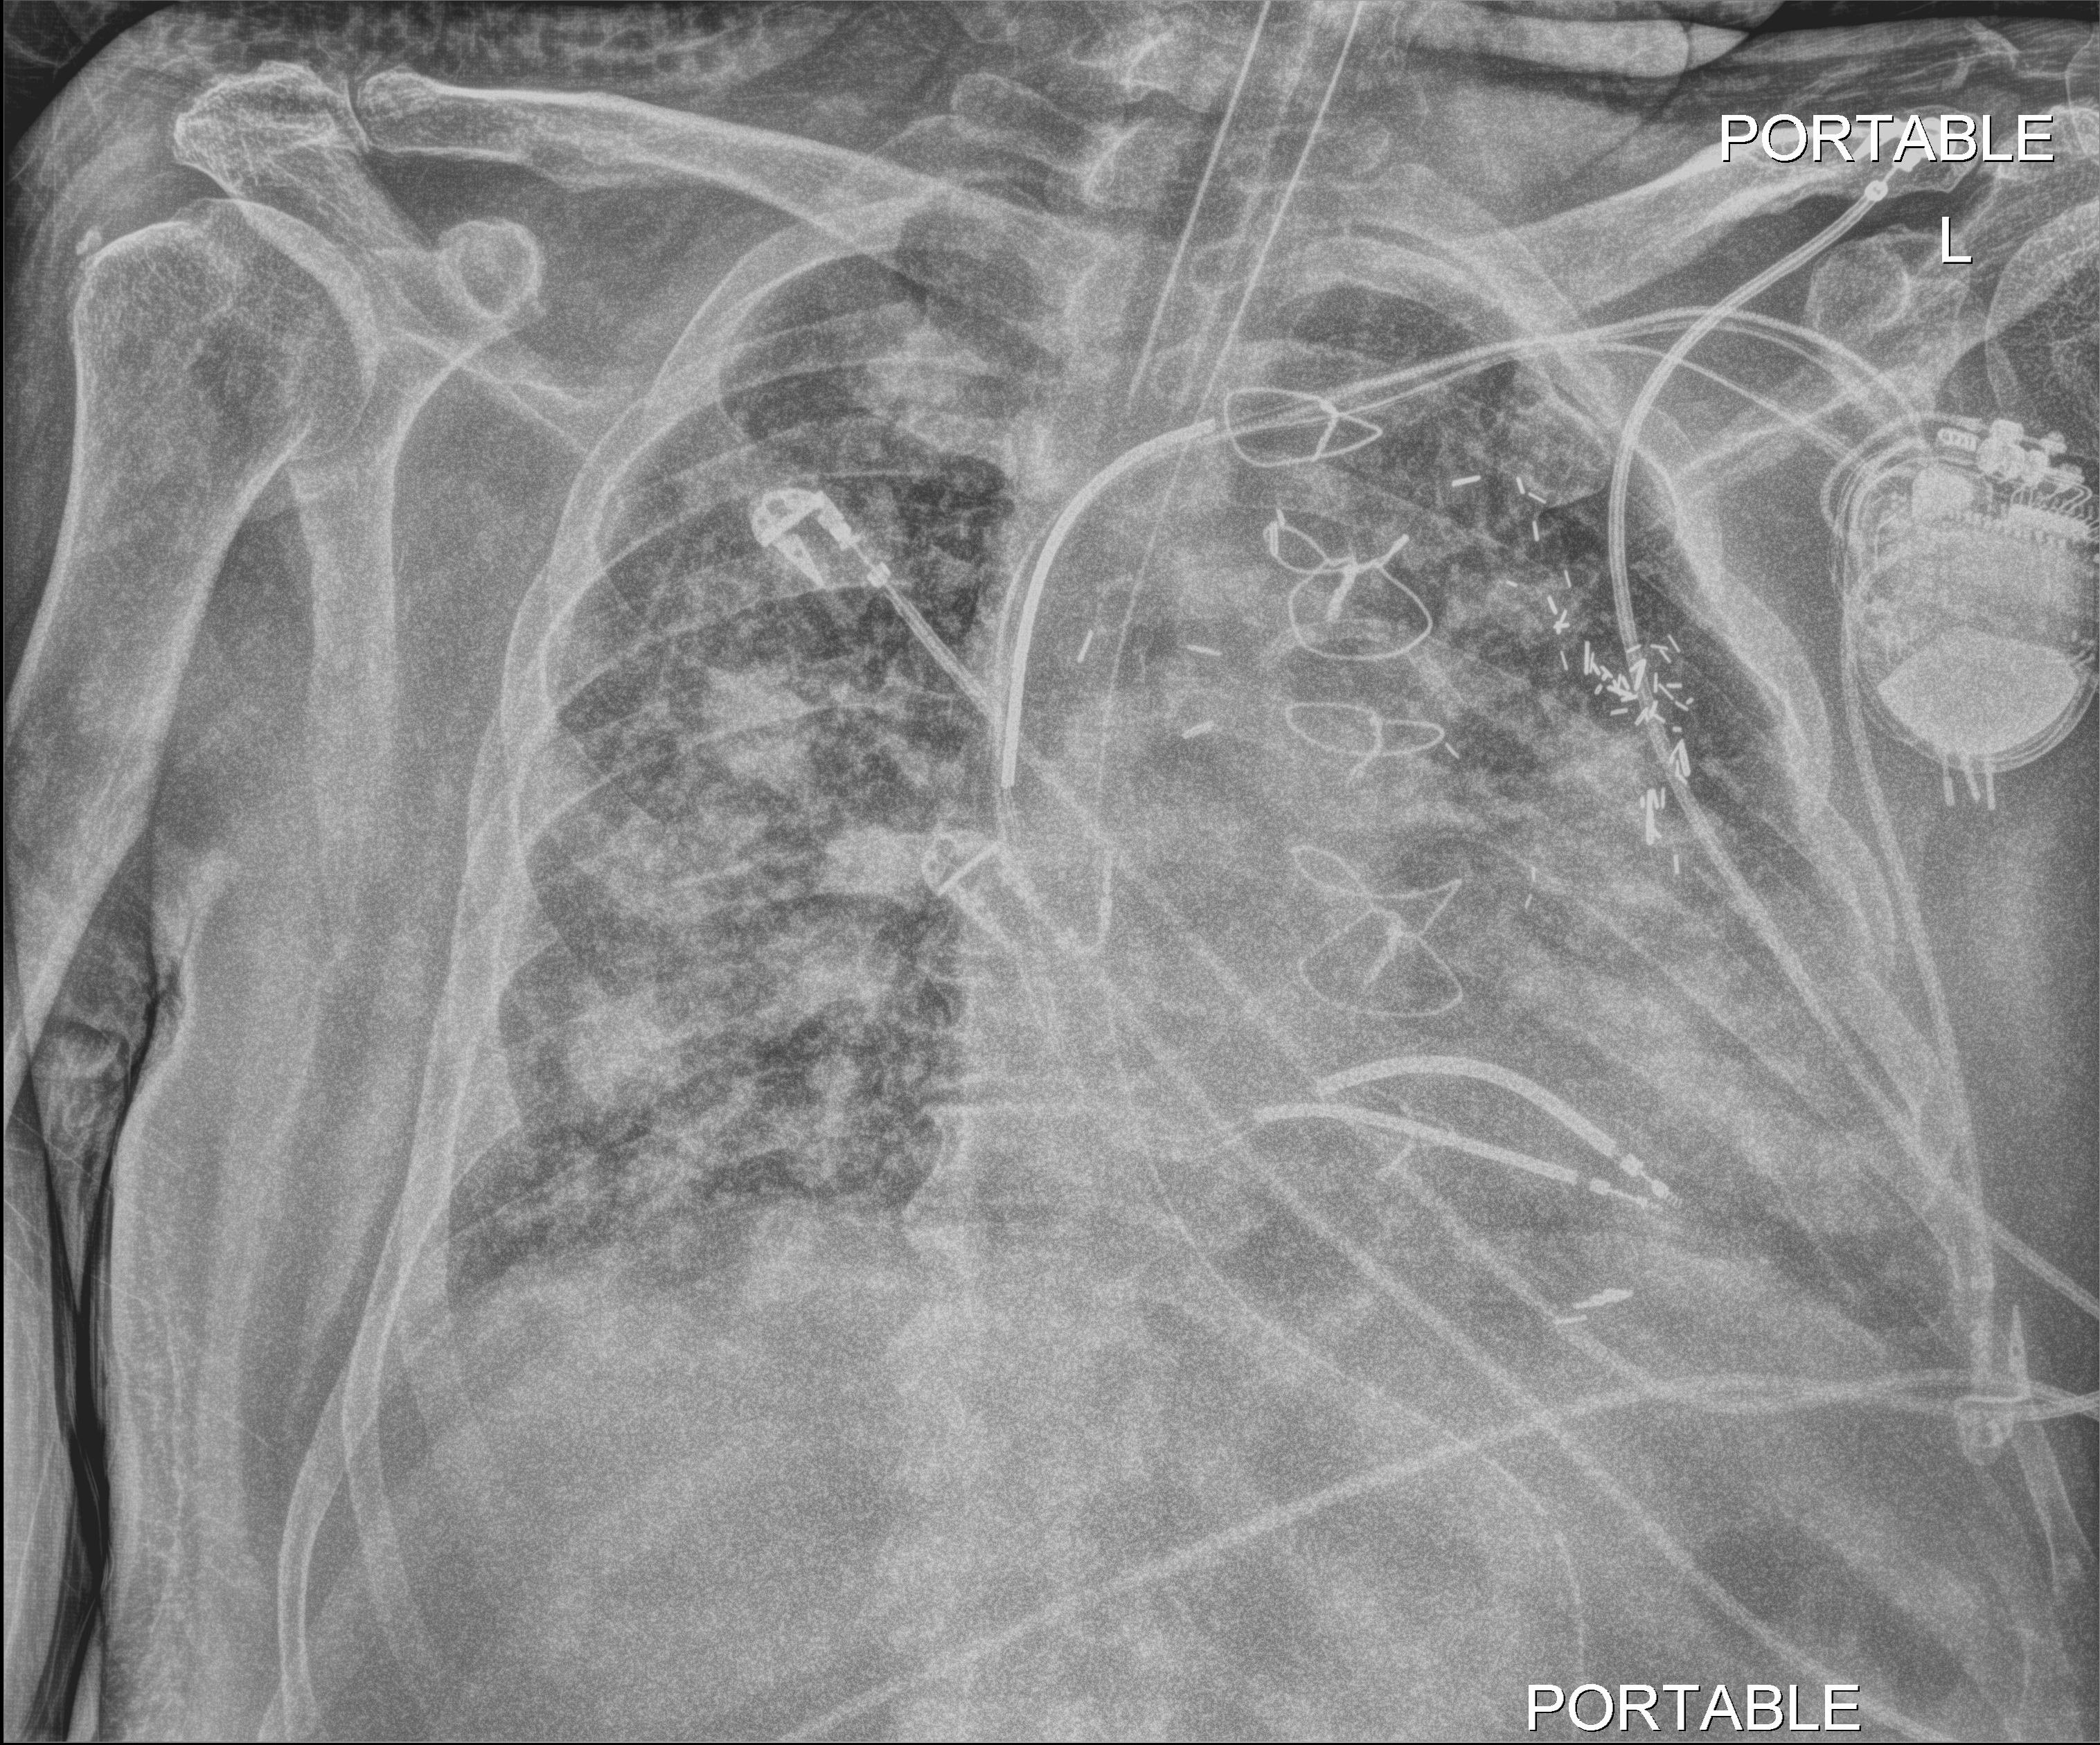
Chest radiograph (digital radiography), anteroposterior (AP) projection. Patient hospitalised with COVID-19; male, aged 60–74 years.
From the hospital-stay record, not from the radiograph (when in the stay this image was taken is not recorded): COPD (admission record): no; admitted to intensive care during this hospital stay: yes.